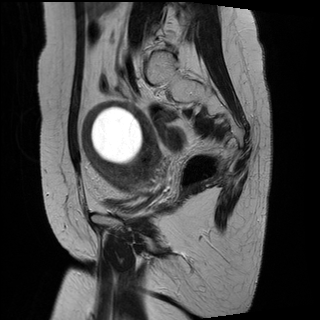
Pelvic MRI for cervical cancer, one sagittal slice. Slice 21 of 29 in the series (ordered by position). T2-weighted. 1.5 T. TE 89 ms, TR 2930 ms. 4 mm slice thickness. 320 × 320 image matrix. Female patient, age 49 years.
Annotated regions visible in this slice (expert manual segmentation):
- uterus and cervix: bounding box [x1, y1, x2, y2] px = [82, 100, 162, 193]